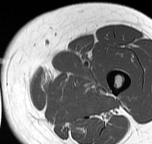
MRI of an extremity soft-tissue mass, one axial slice; position 12 of 57 along the scan axis; MR volume resampled by the dataset authors to the PET/CT grid (not the native acquisition matrix); 152 × 144 image matrix, field of view 148 × 141 mm. Female patient. From the clinical record (not read from this slice): histological type: pleiomorphic leiomyosarcoma; grade: intermediate; site of the primary tumour: left thigh.
Annotated regions visible in this slice (expert contour drawn on MRI and transferred to this co-registered scan by the dataset authors):
- gross tumour volume including surrounding oedema: bounding box (x1, y1, x2, y2) in pixels: (41, 69, 103, 93)